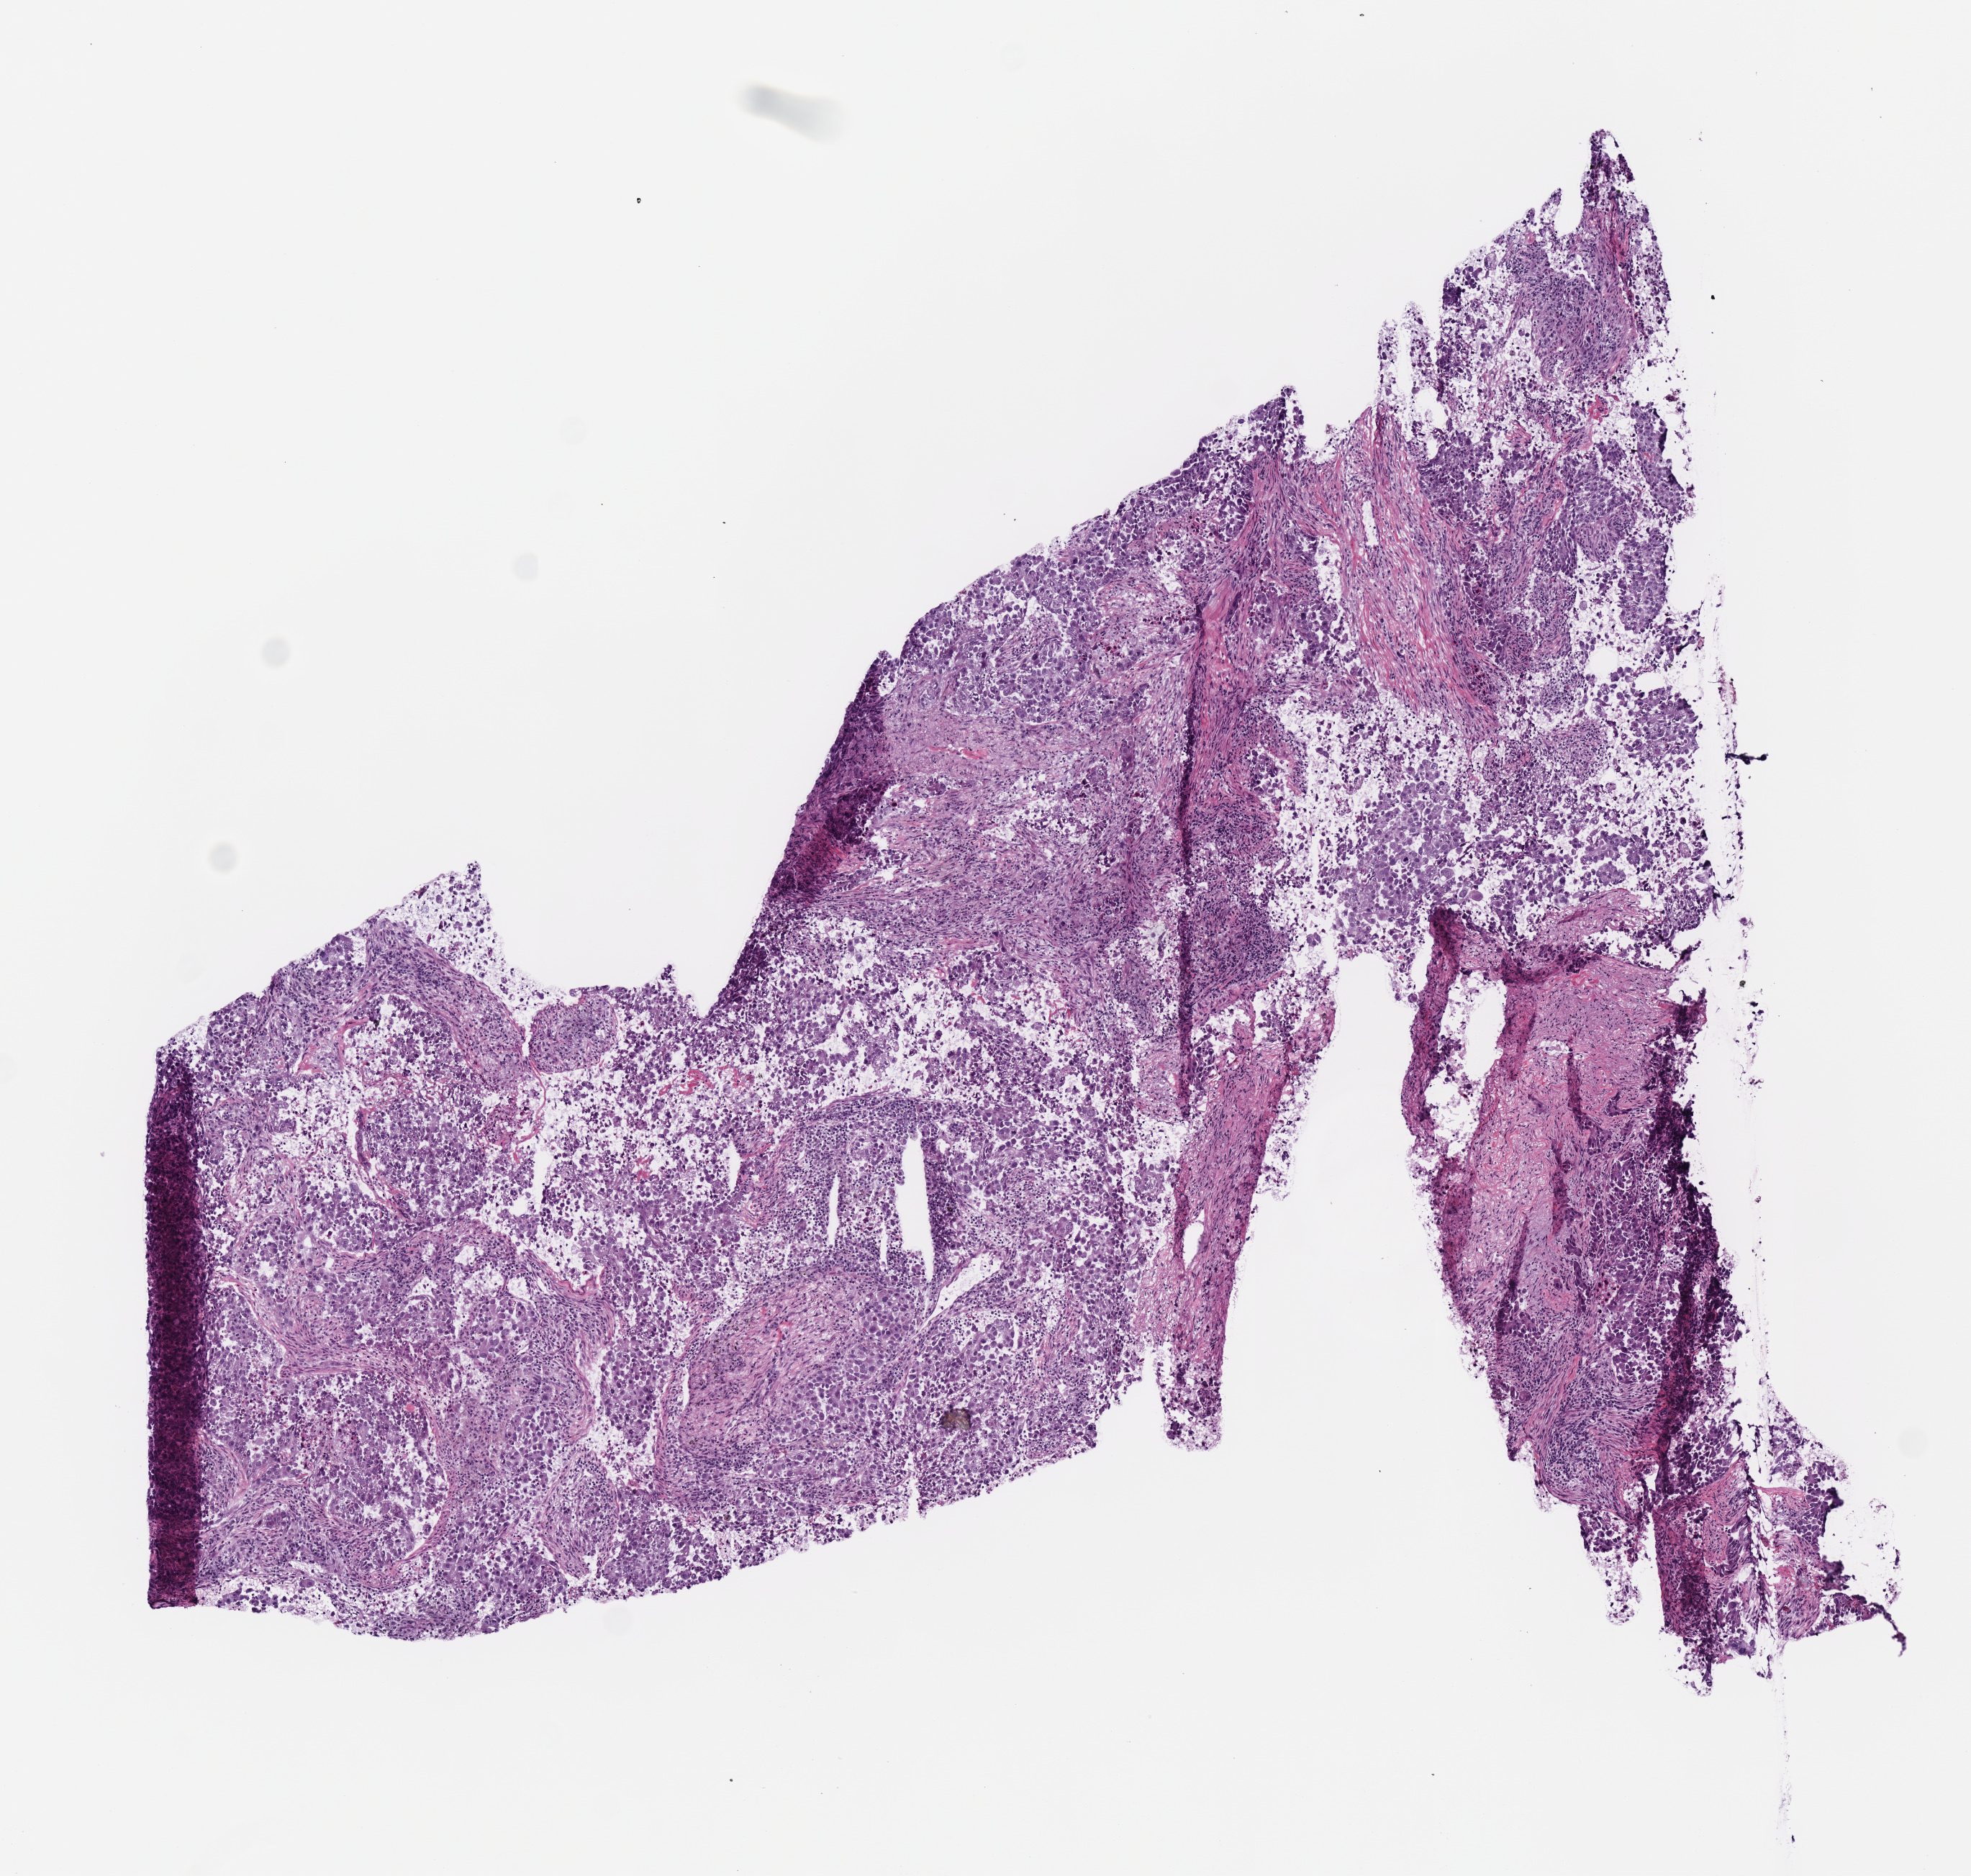
H&E whole-slide image — a low-resolution overview of the entire scanned area, about 5.4 x 5.1 mm (from a 40x scan), frozen section from the top of the tissue portion, sample: primary tumour, lung. Patient: male, age at initial diagnosis 61 years. Slide review estimates, as recorded: tumour cells 85%, tumour nuclei 65%, normal cells 0%, stromal cells 15%, necrosis 0%.
AJCC pathologic stage: IB (7th edition). Histologic diagnosis: Adenocarcinoma, NOS.